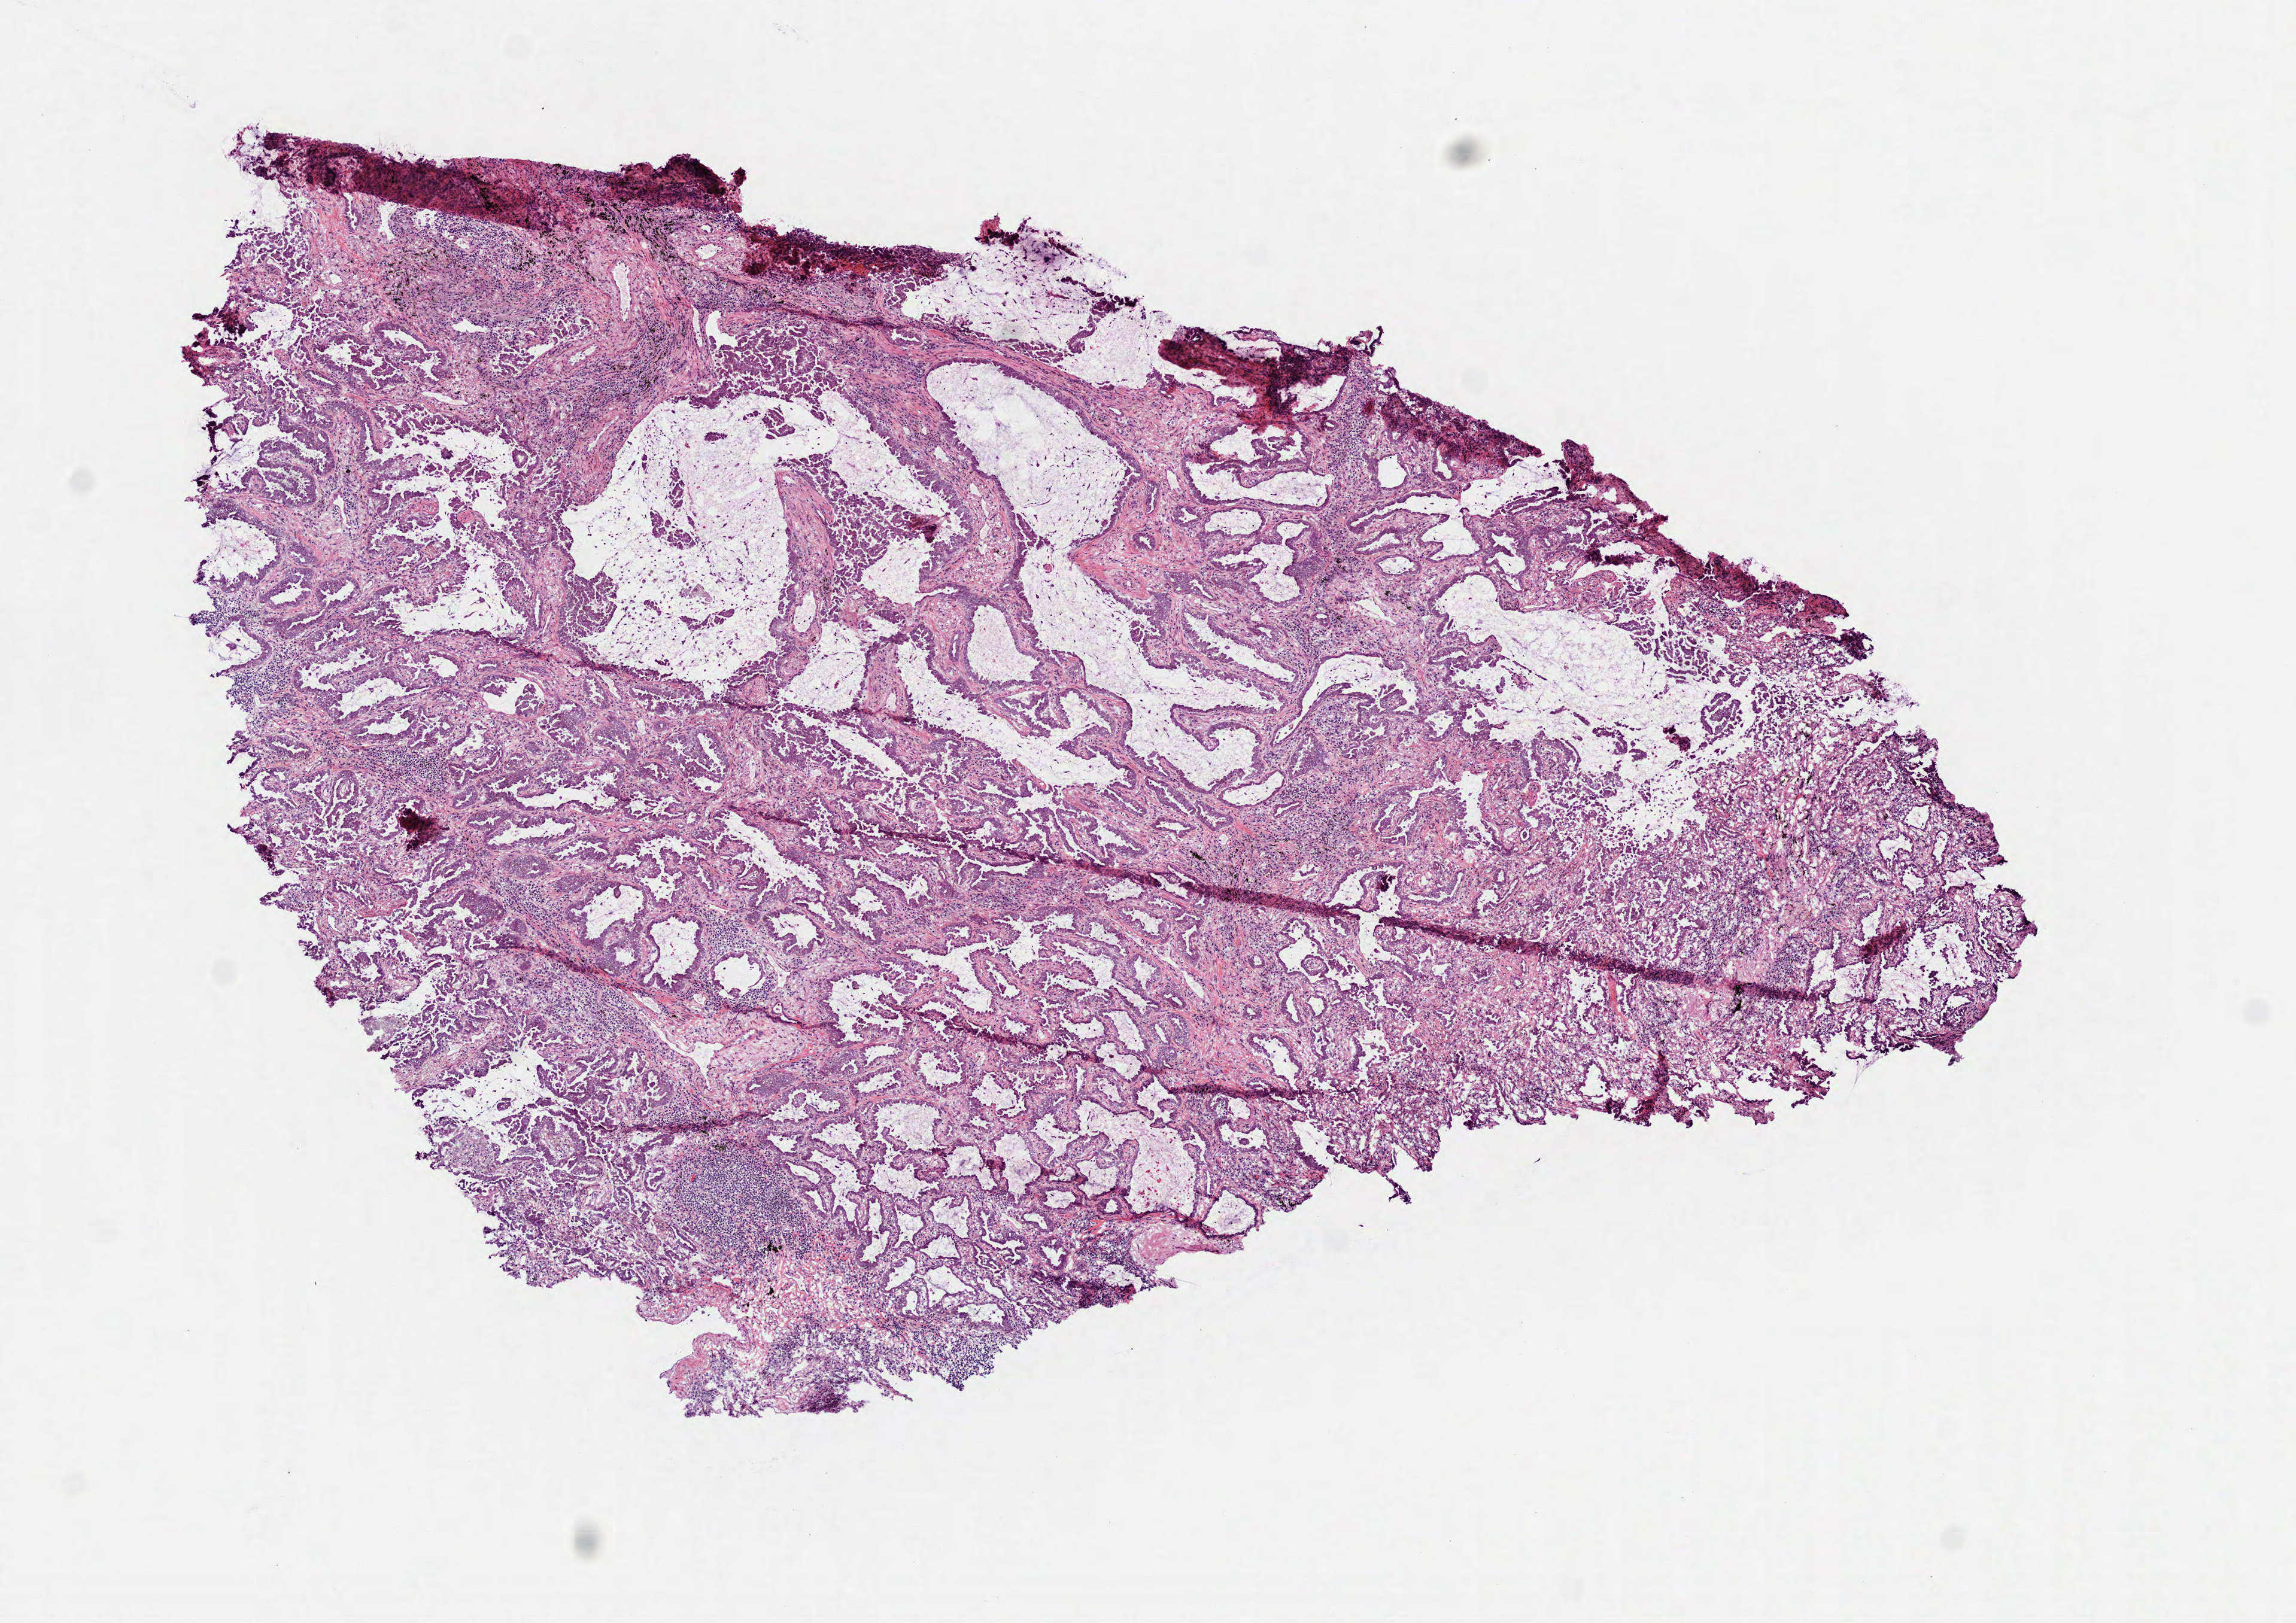
Whole-slide histology image, H&E-stained — shown as a low-resolution overview of the whole scanned area (about 7.7 x 5.5 mm). Frozen section from the top of the tissue portion. Lung, primary tumour sample. Male patient; age at initial diagnosis 65 years. Slide review estimates, as recorded: tumour cells 80%, tumour nuclei 60%, normal cells 0%, stromal cells 20%, necrosis 0%.
• laterality: right
• AJCC pathologic stage: IB
• TNM: T2 N0 M0
• pathologic diagnosis: Adenocarcinoma with mixed subtypes (upper lobe, lung)